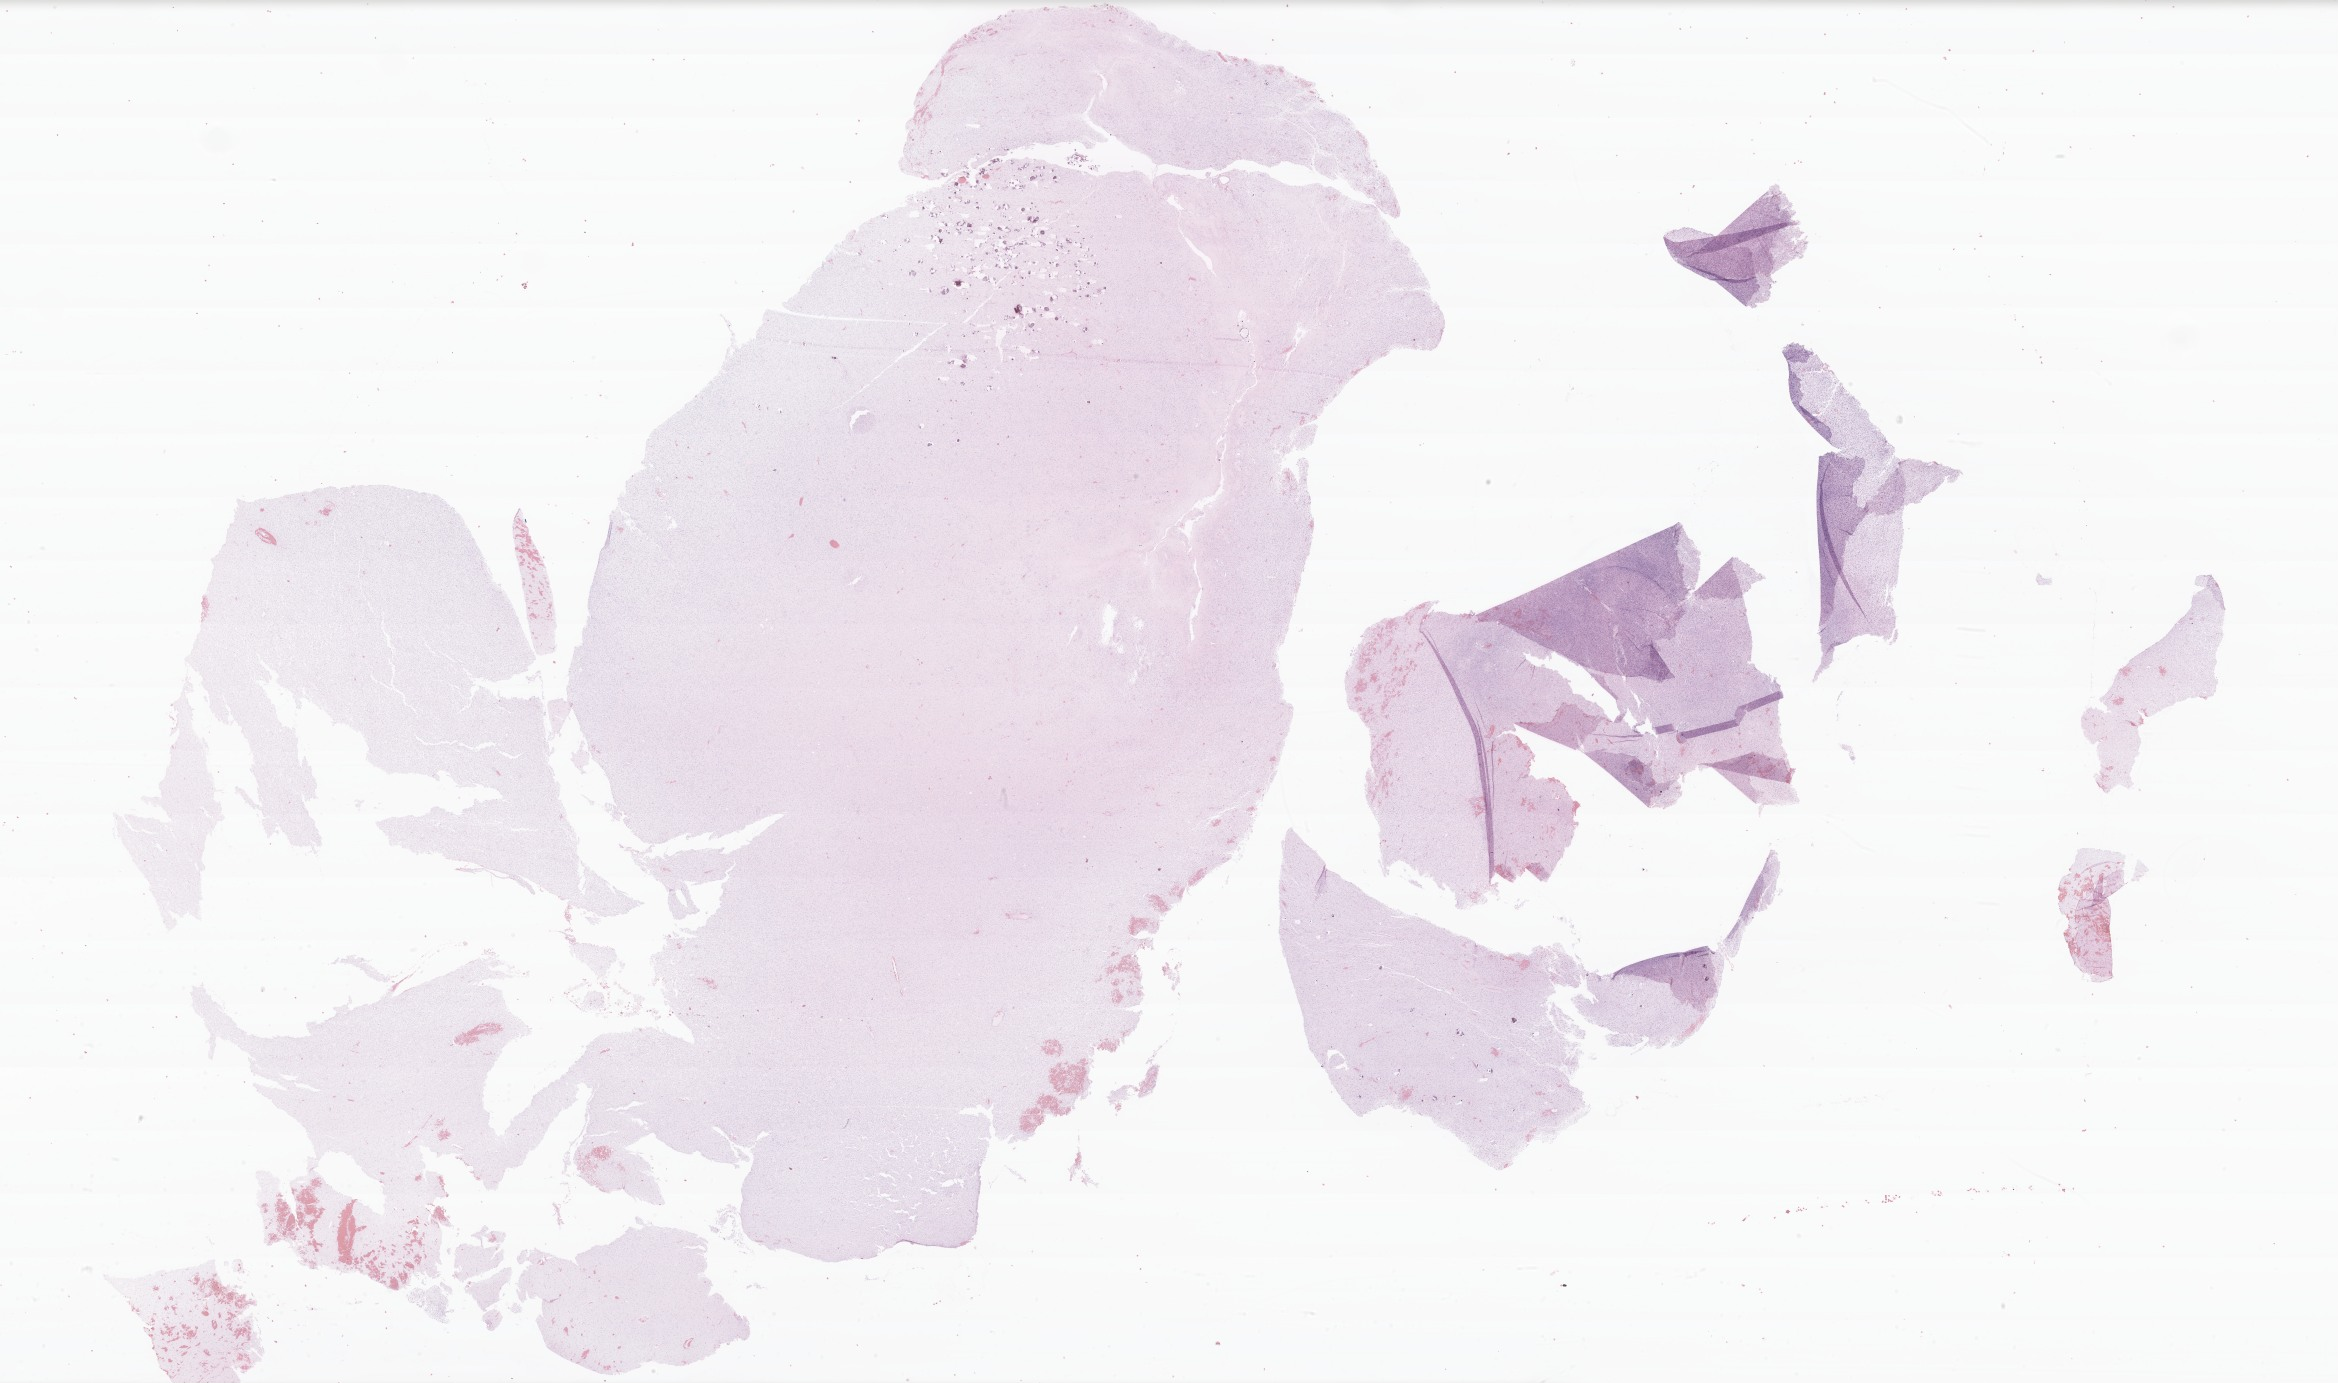
Digitized hematoxylin and eosin (H&E)-stained section of tumor tissue from the cerebrum — shown as a low-resolution overview of the whole scanned area (about 39.3 x 23.3 mm). FFPE section. Male patient, age 181 months (15 years 1 month).
• diagnosis: Glioblastoma, NOS